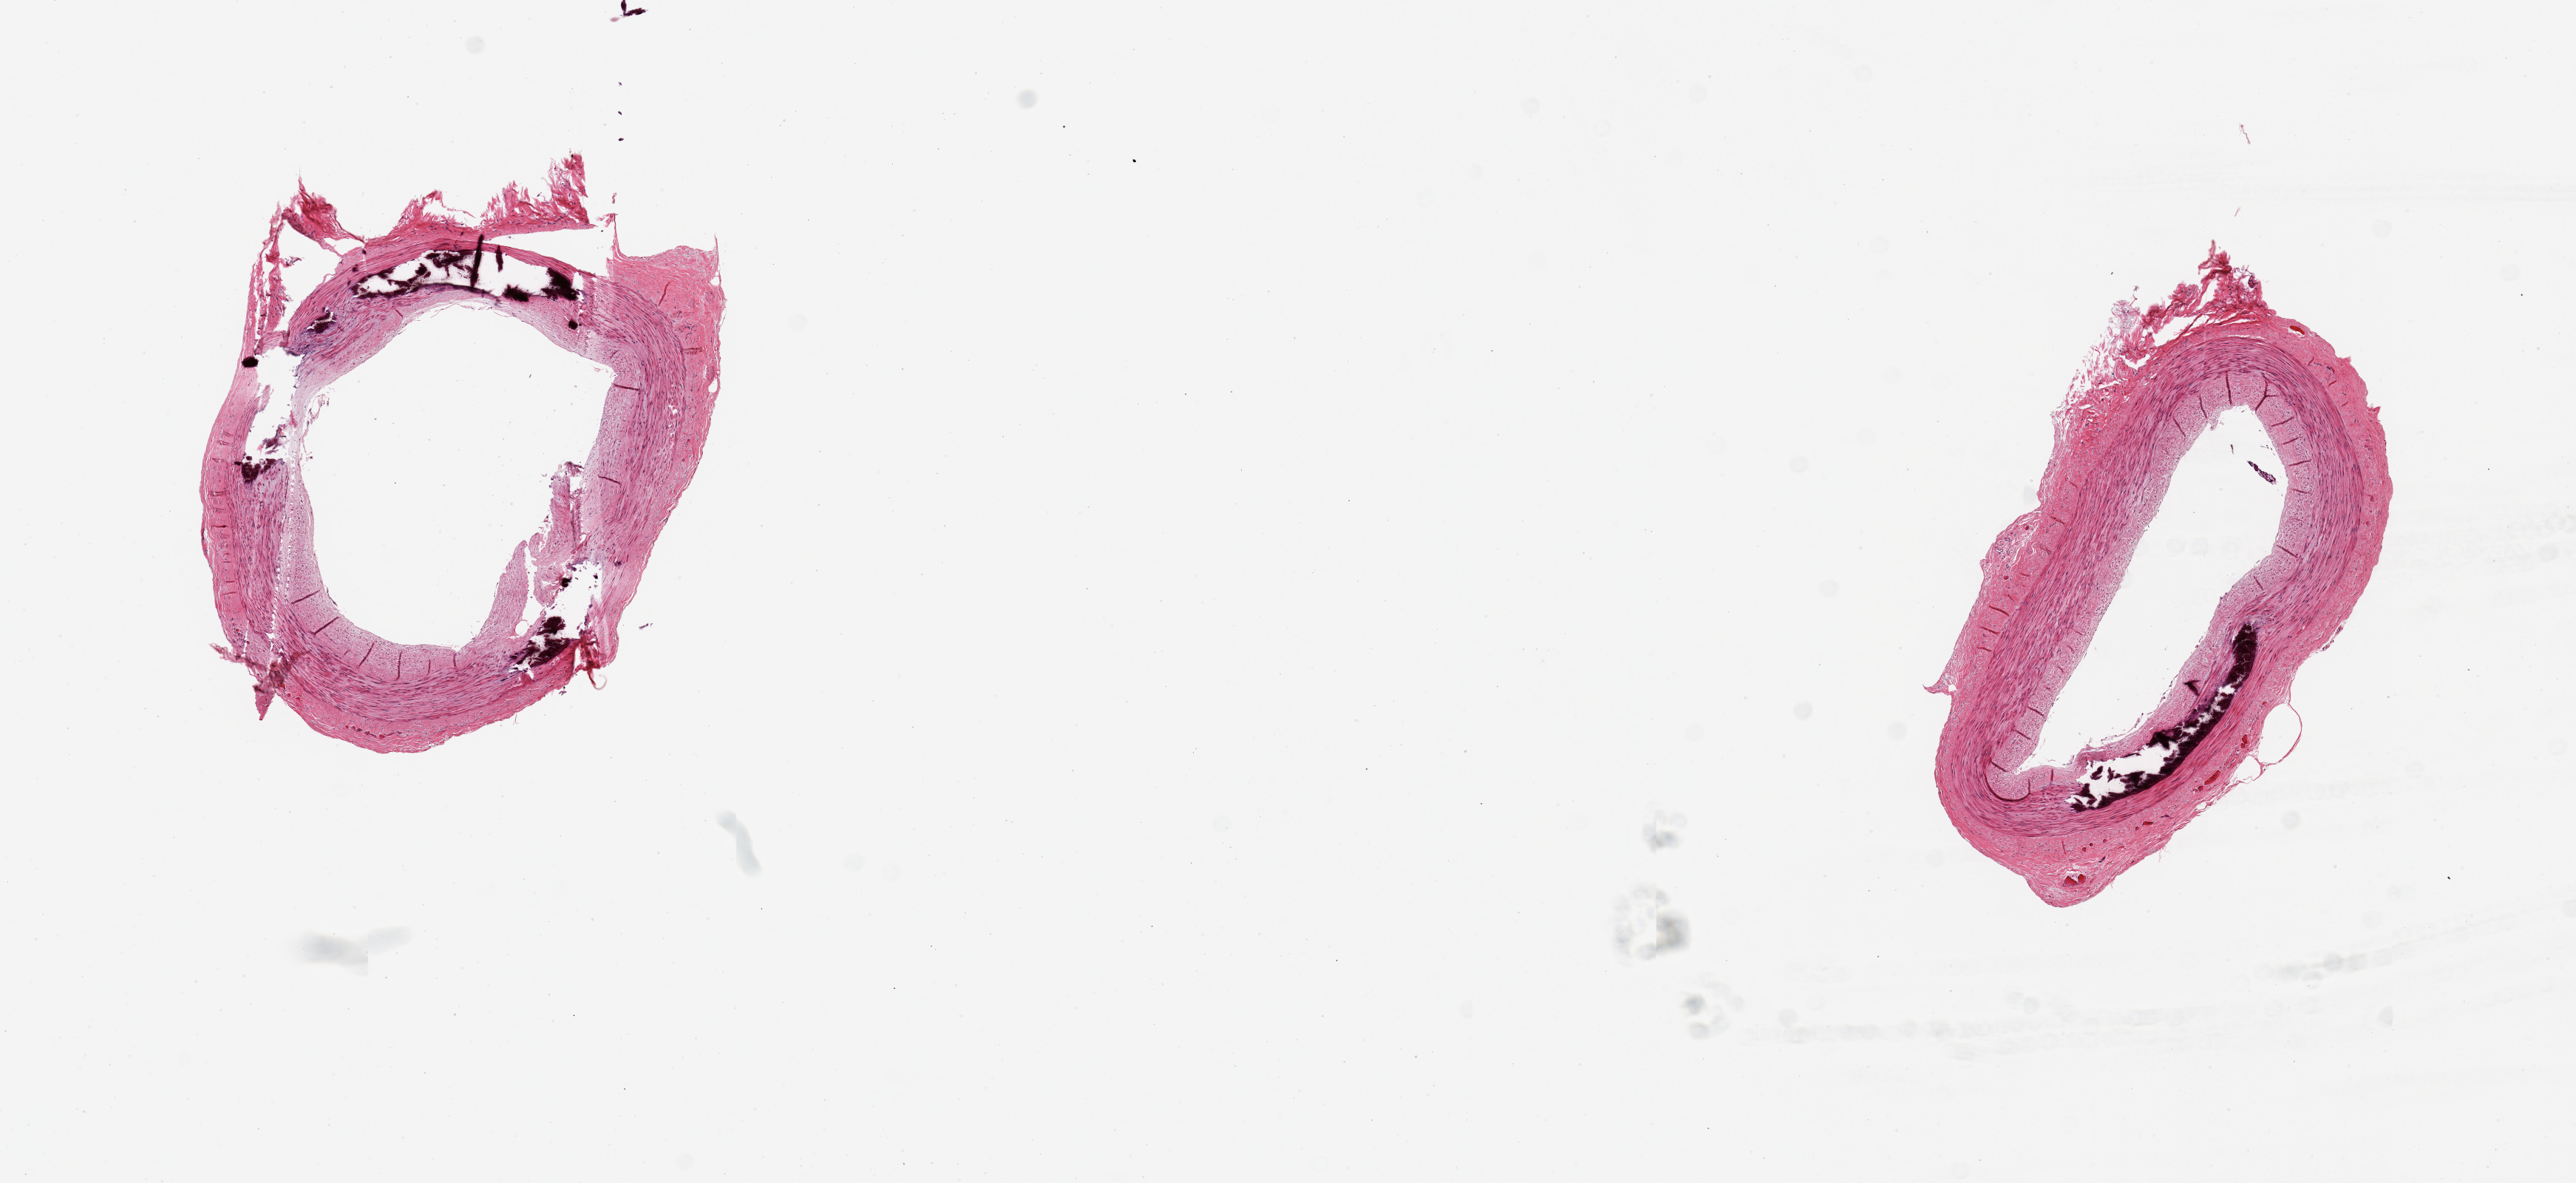
Haematoxylin and eosin whole-slide image — low-resolution overview of the scanned area, about 13.8 x 6.3 mm, PAXgene-fixed, paraffin-embedded tissue, sampled site (target tissue): tibial artery, donor tissue sample. Donor: male.
Reviewer comment on this tissue sample: 2 pieces; atheromatous change and medial calcifications.